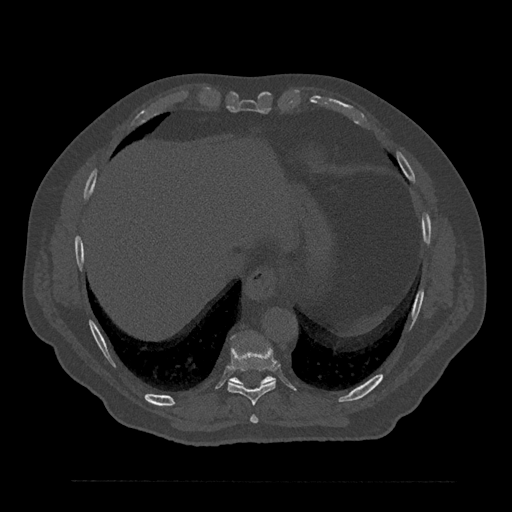
CT including the spine, one axial slice. Position 391 of 797 along the scan axis. 120 kVp. Bone window (W 1800 / L 400 HU). 0.5 mm slice thickness. 512 × 512 image matrix, field of view 430 × 430 mm. Patient: male, 61 years. From the clinical record (not read from this slice): primary cancer: prostate.
Annotated regions visible in this slice (semi-automatic segmentation, software-assisted and operator-edited):
- T10 vertebra: bounding box (x1, y1, x2, y2) in pixels: (228, 376, 274, 387)
- T8 vertebra: (250, 415, 259, 424)
- T9 vertebra: (227, 336, 277, 406)